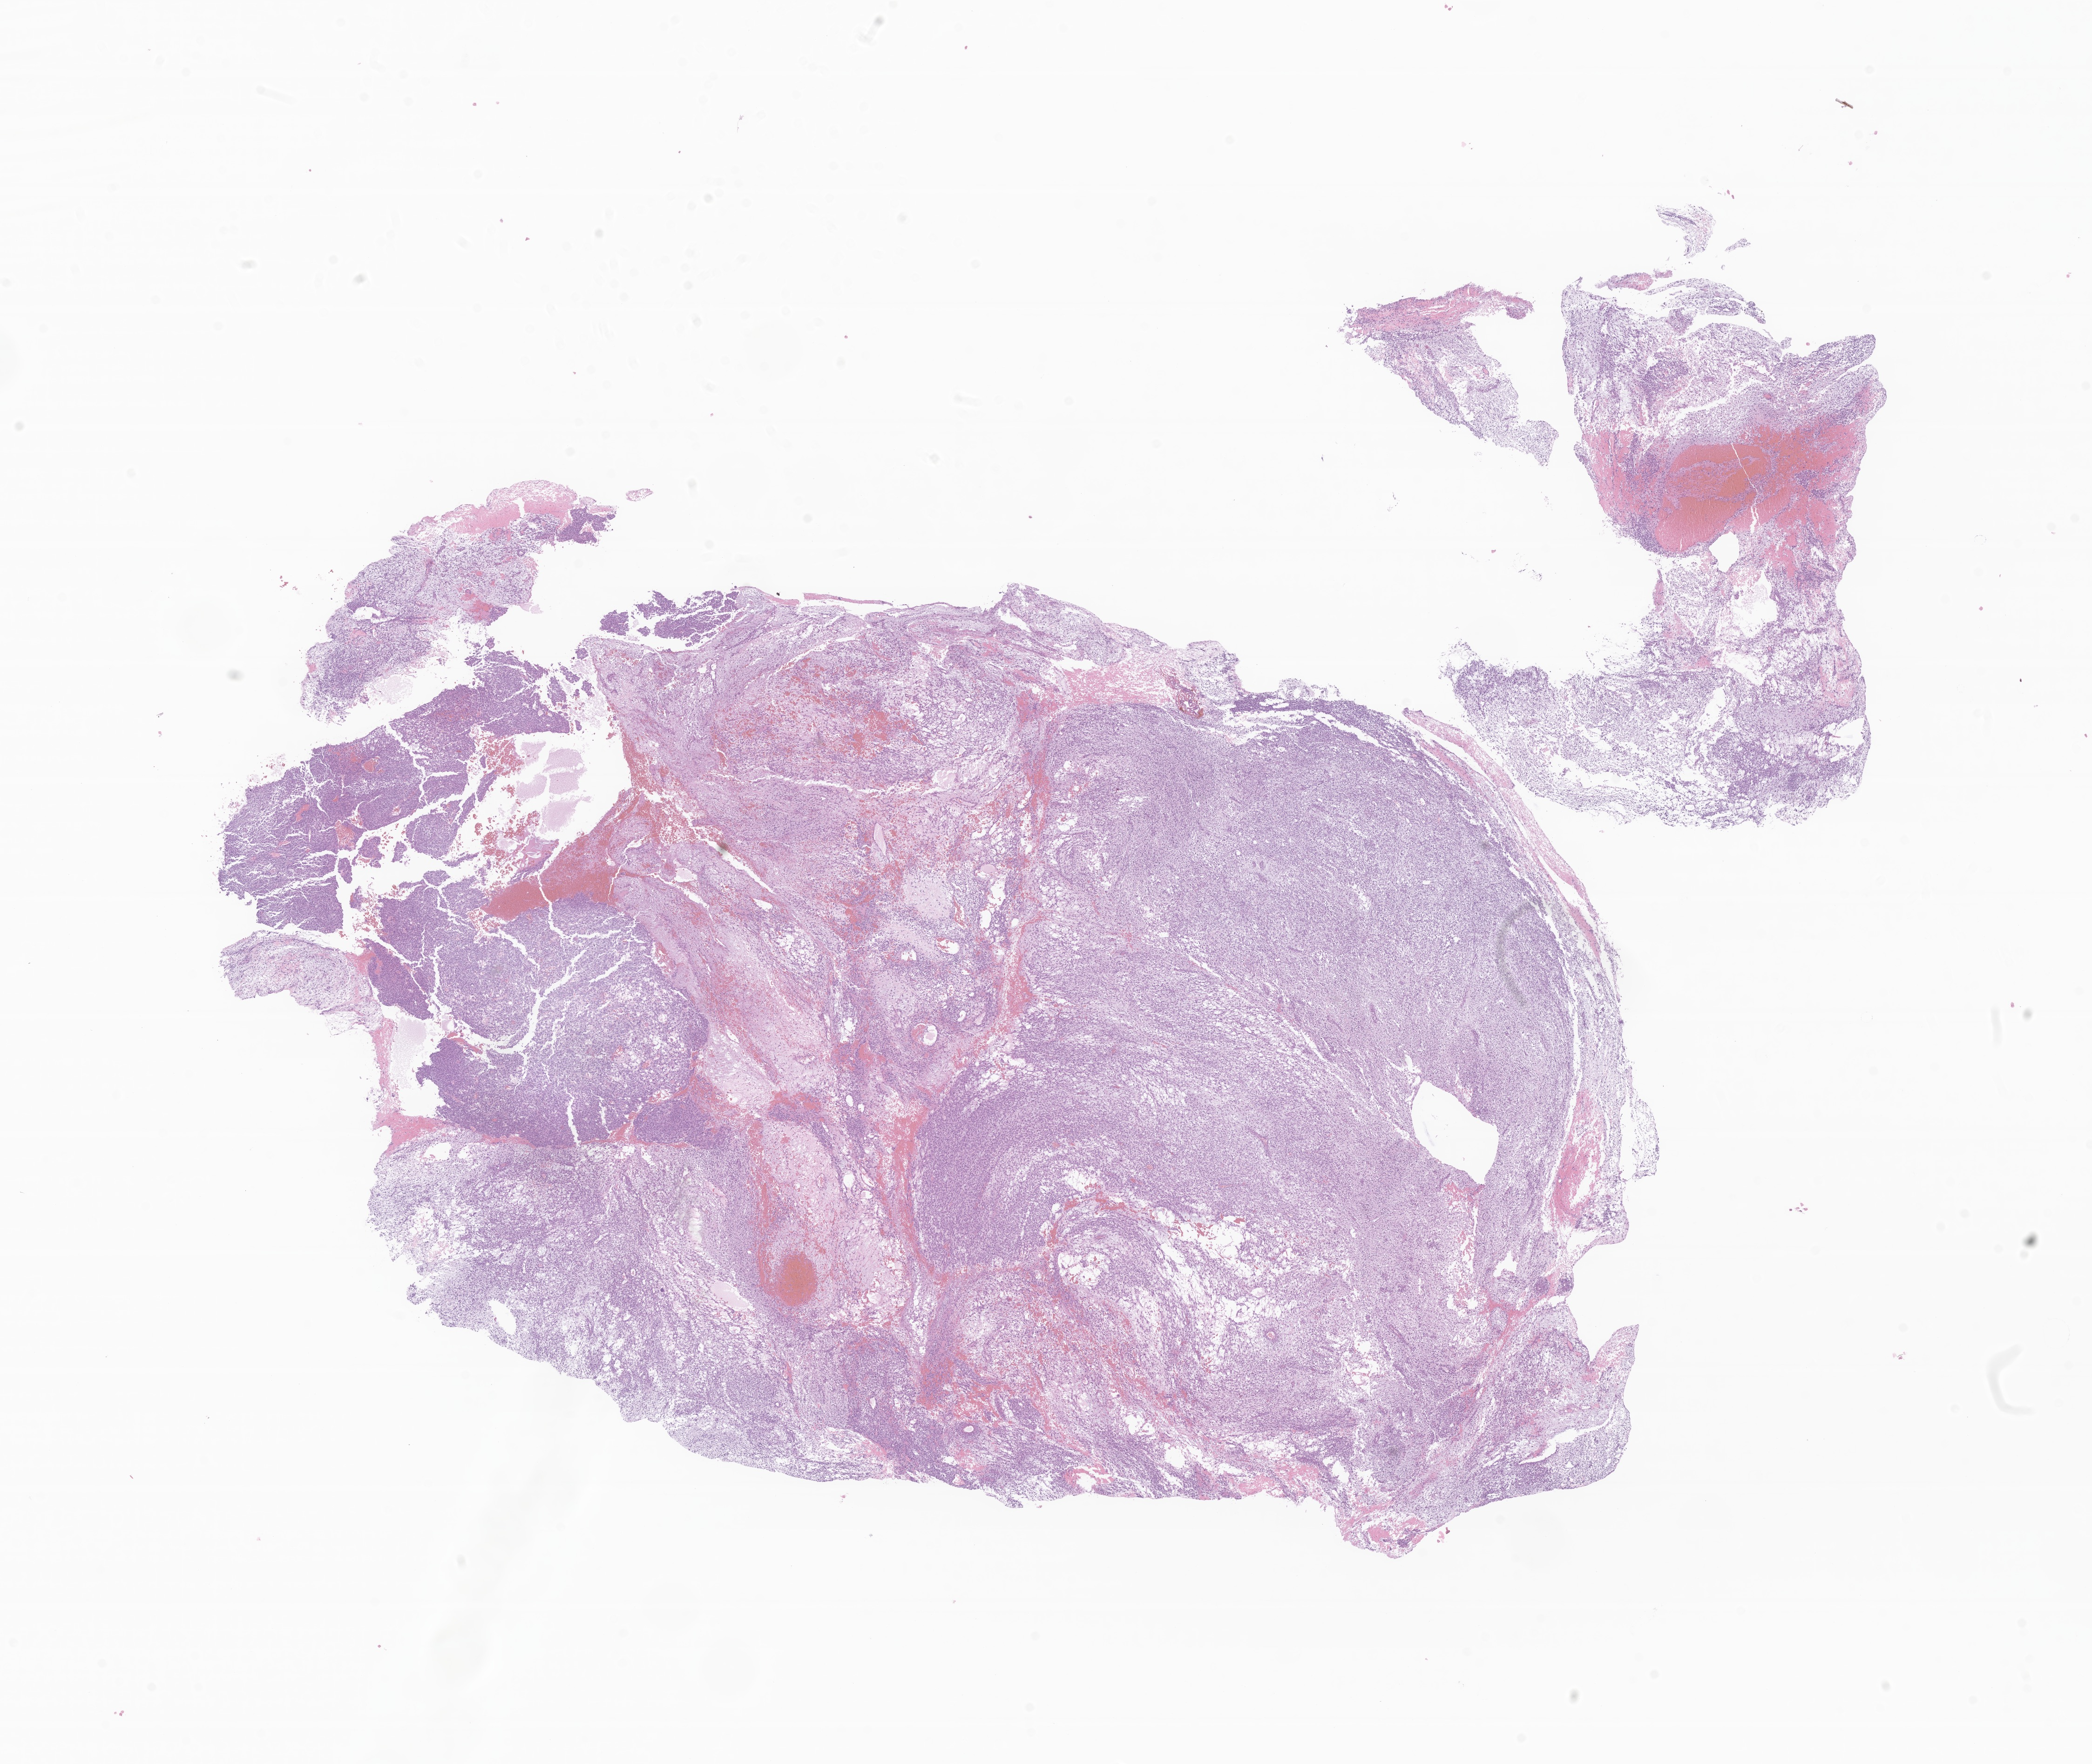
Whole-slide image, hematoxylin and eosin (H&E) stain of tumor tissue from the liver, shown as a low-resolution overview of the whole scanned area (about 18.9 x 16.0 mm). Formalin-fixed paraffin-embedded section. Male patient, age 57 months (4 years 9 months).
Recorded diagnosis: Undifferentiated sarcoma.